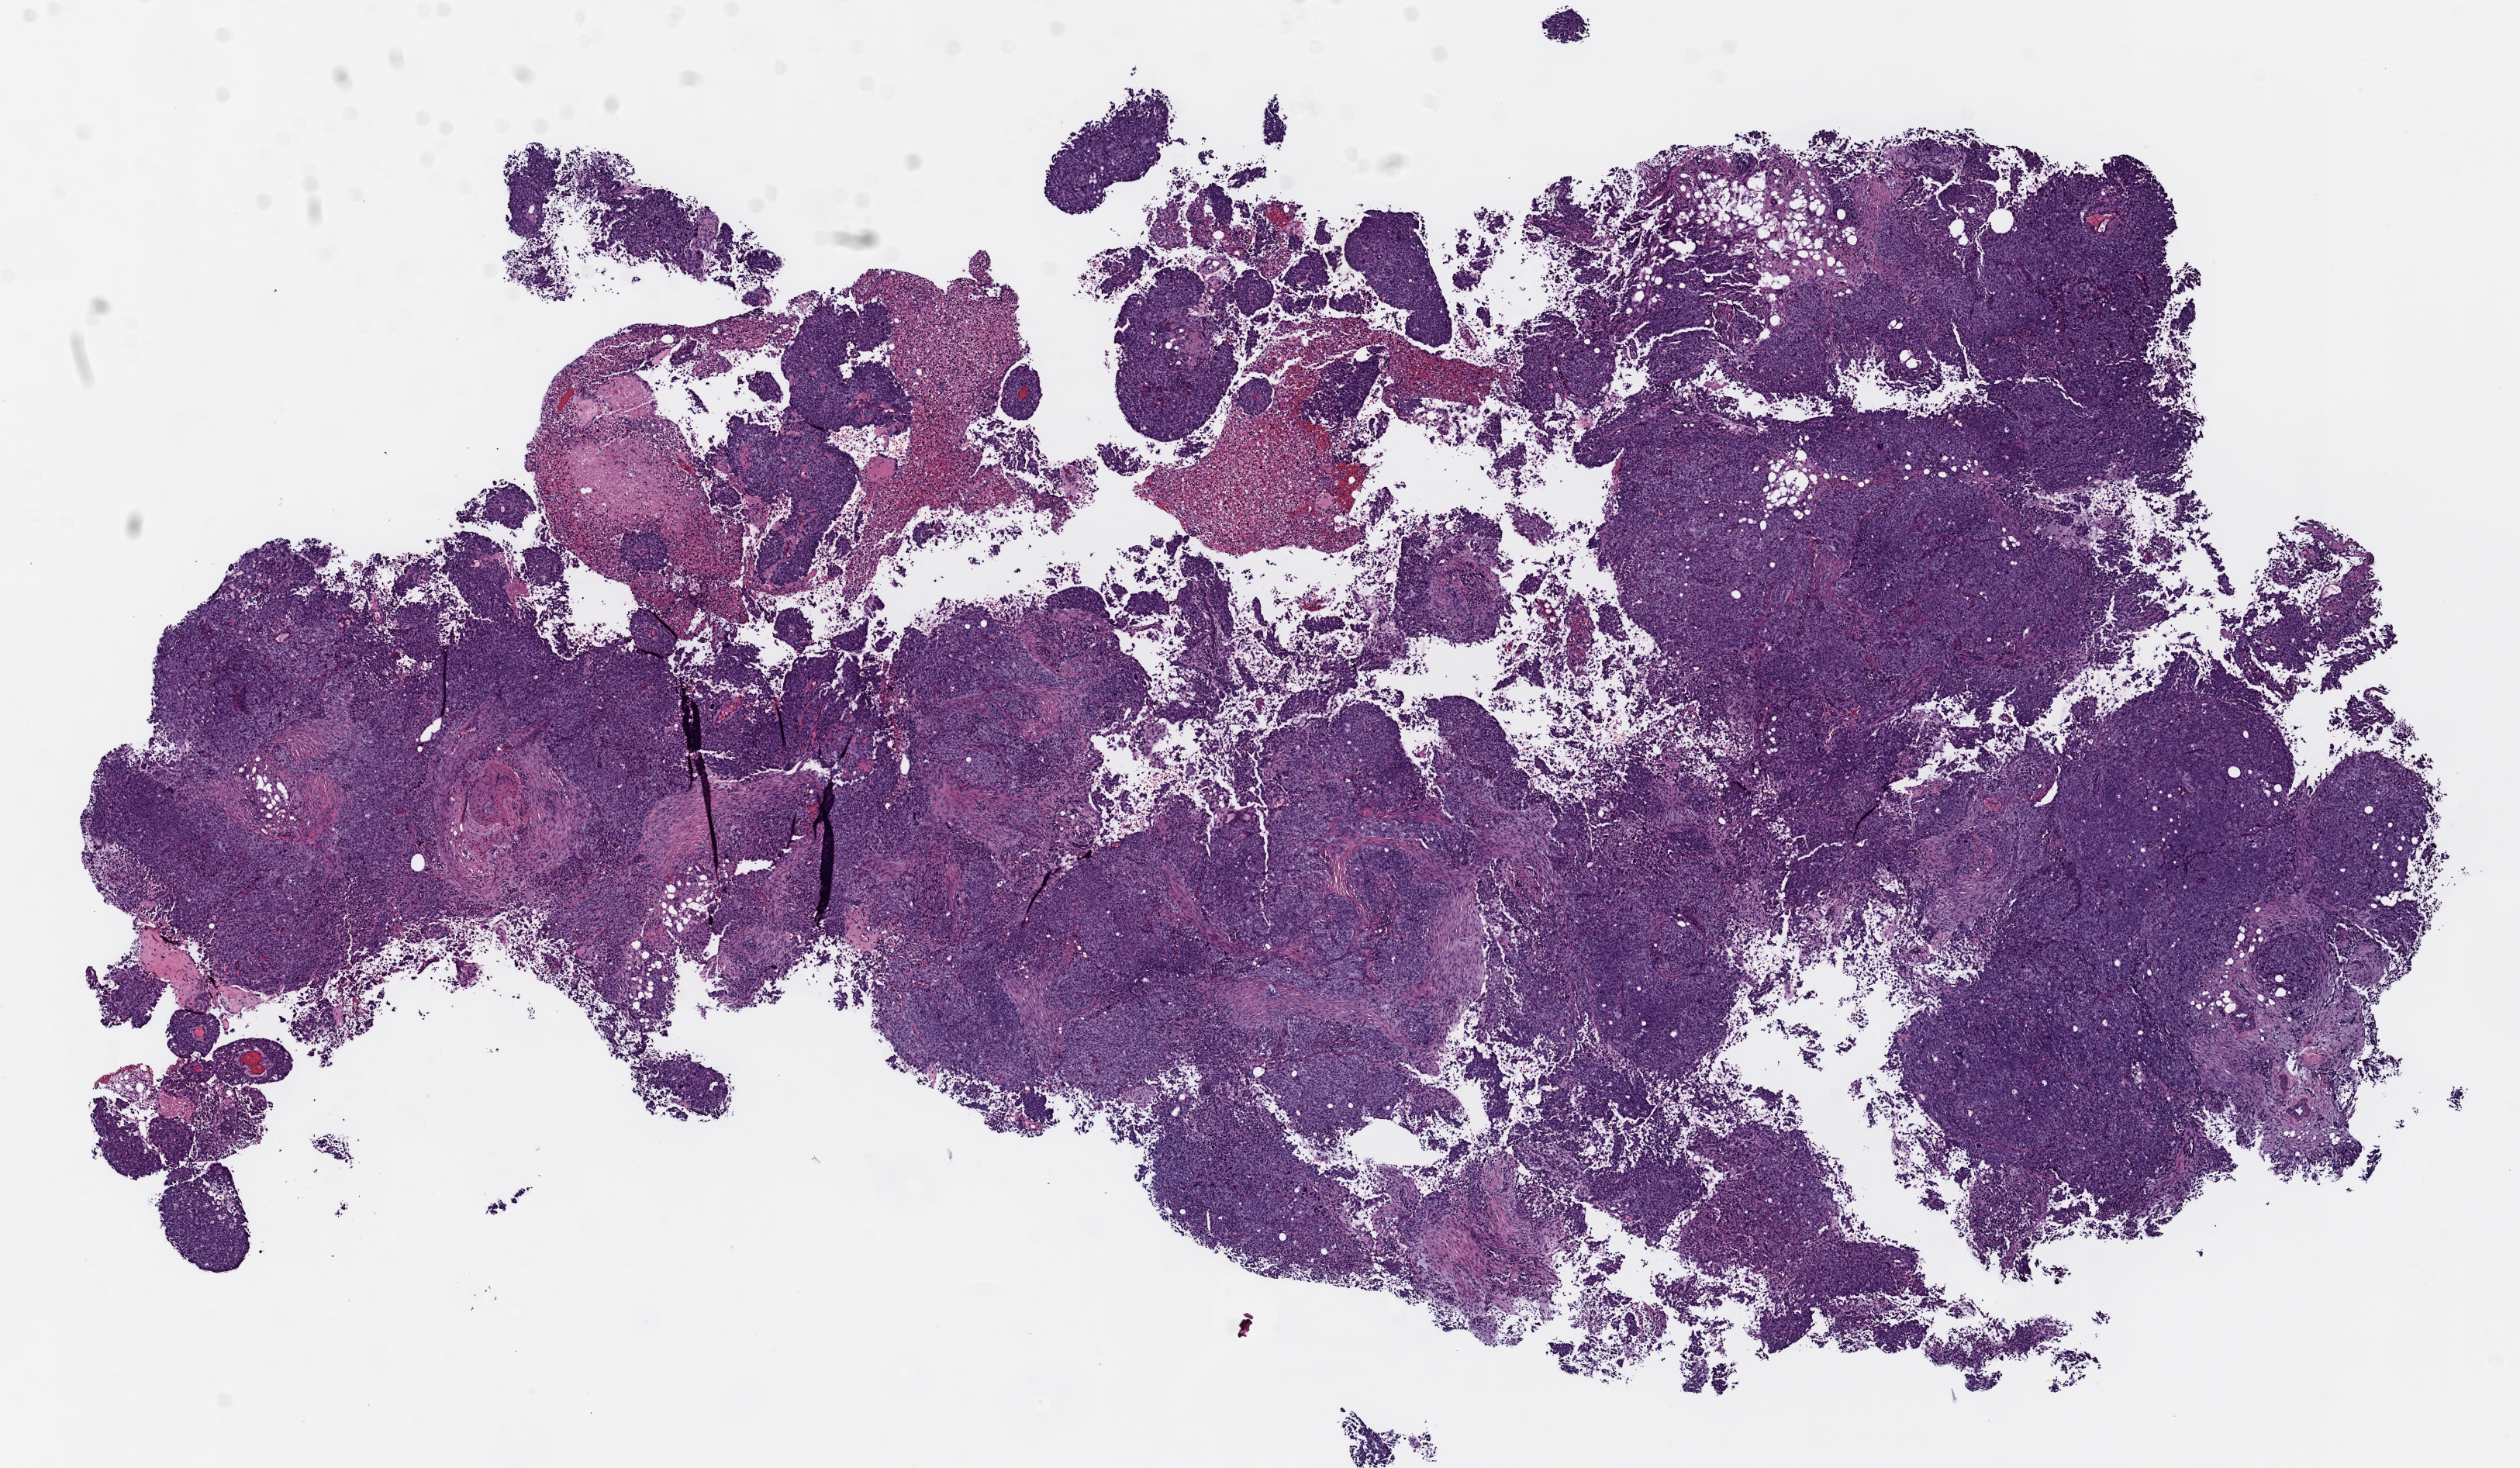
H&E whole-slide image — whole scanned area (about 13.0 x 7.6 mm) shown as a low-resolution overview. Frozen section from the top of the tissue portion. Sample: primary tumour, ovary. Female patient; age at initial diagnosis 75 years.
Diagnosis: Serous cystadenocarcinoma, NOS.